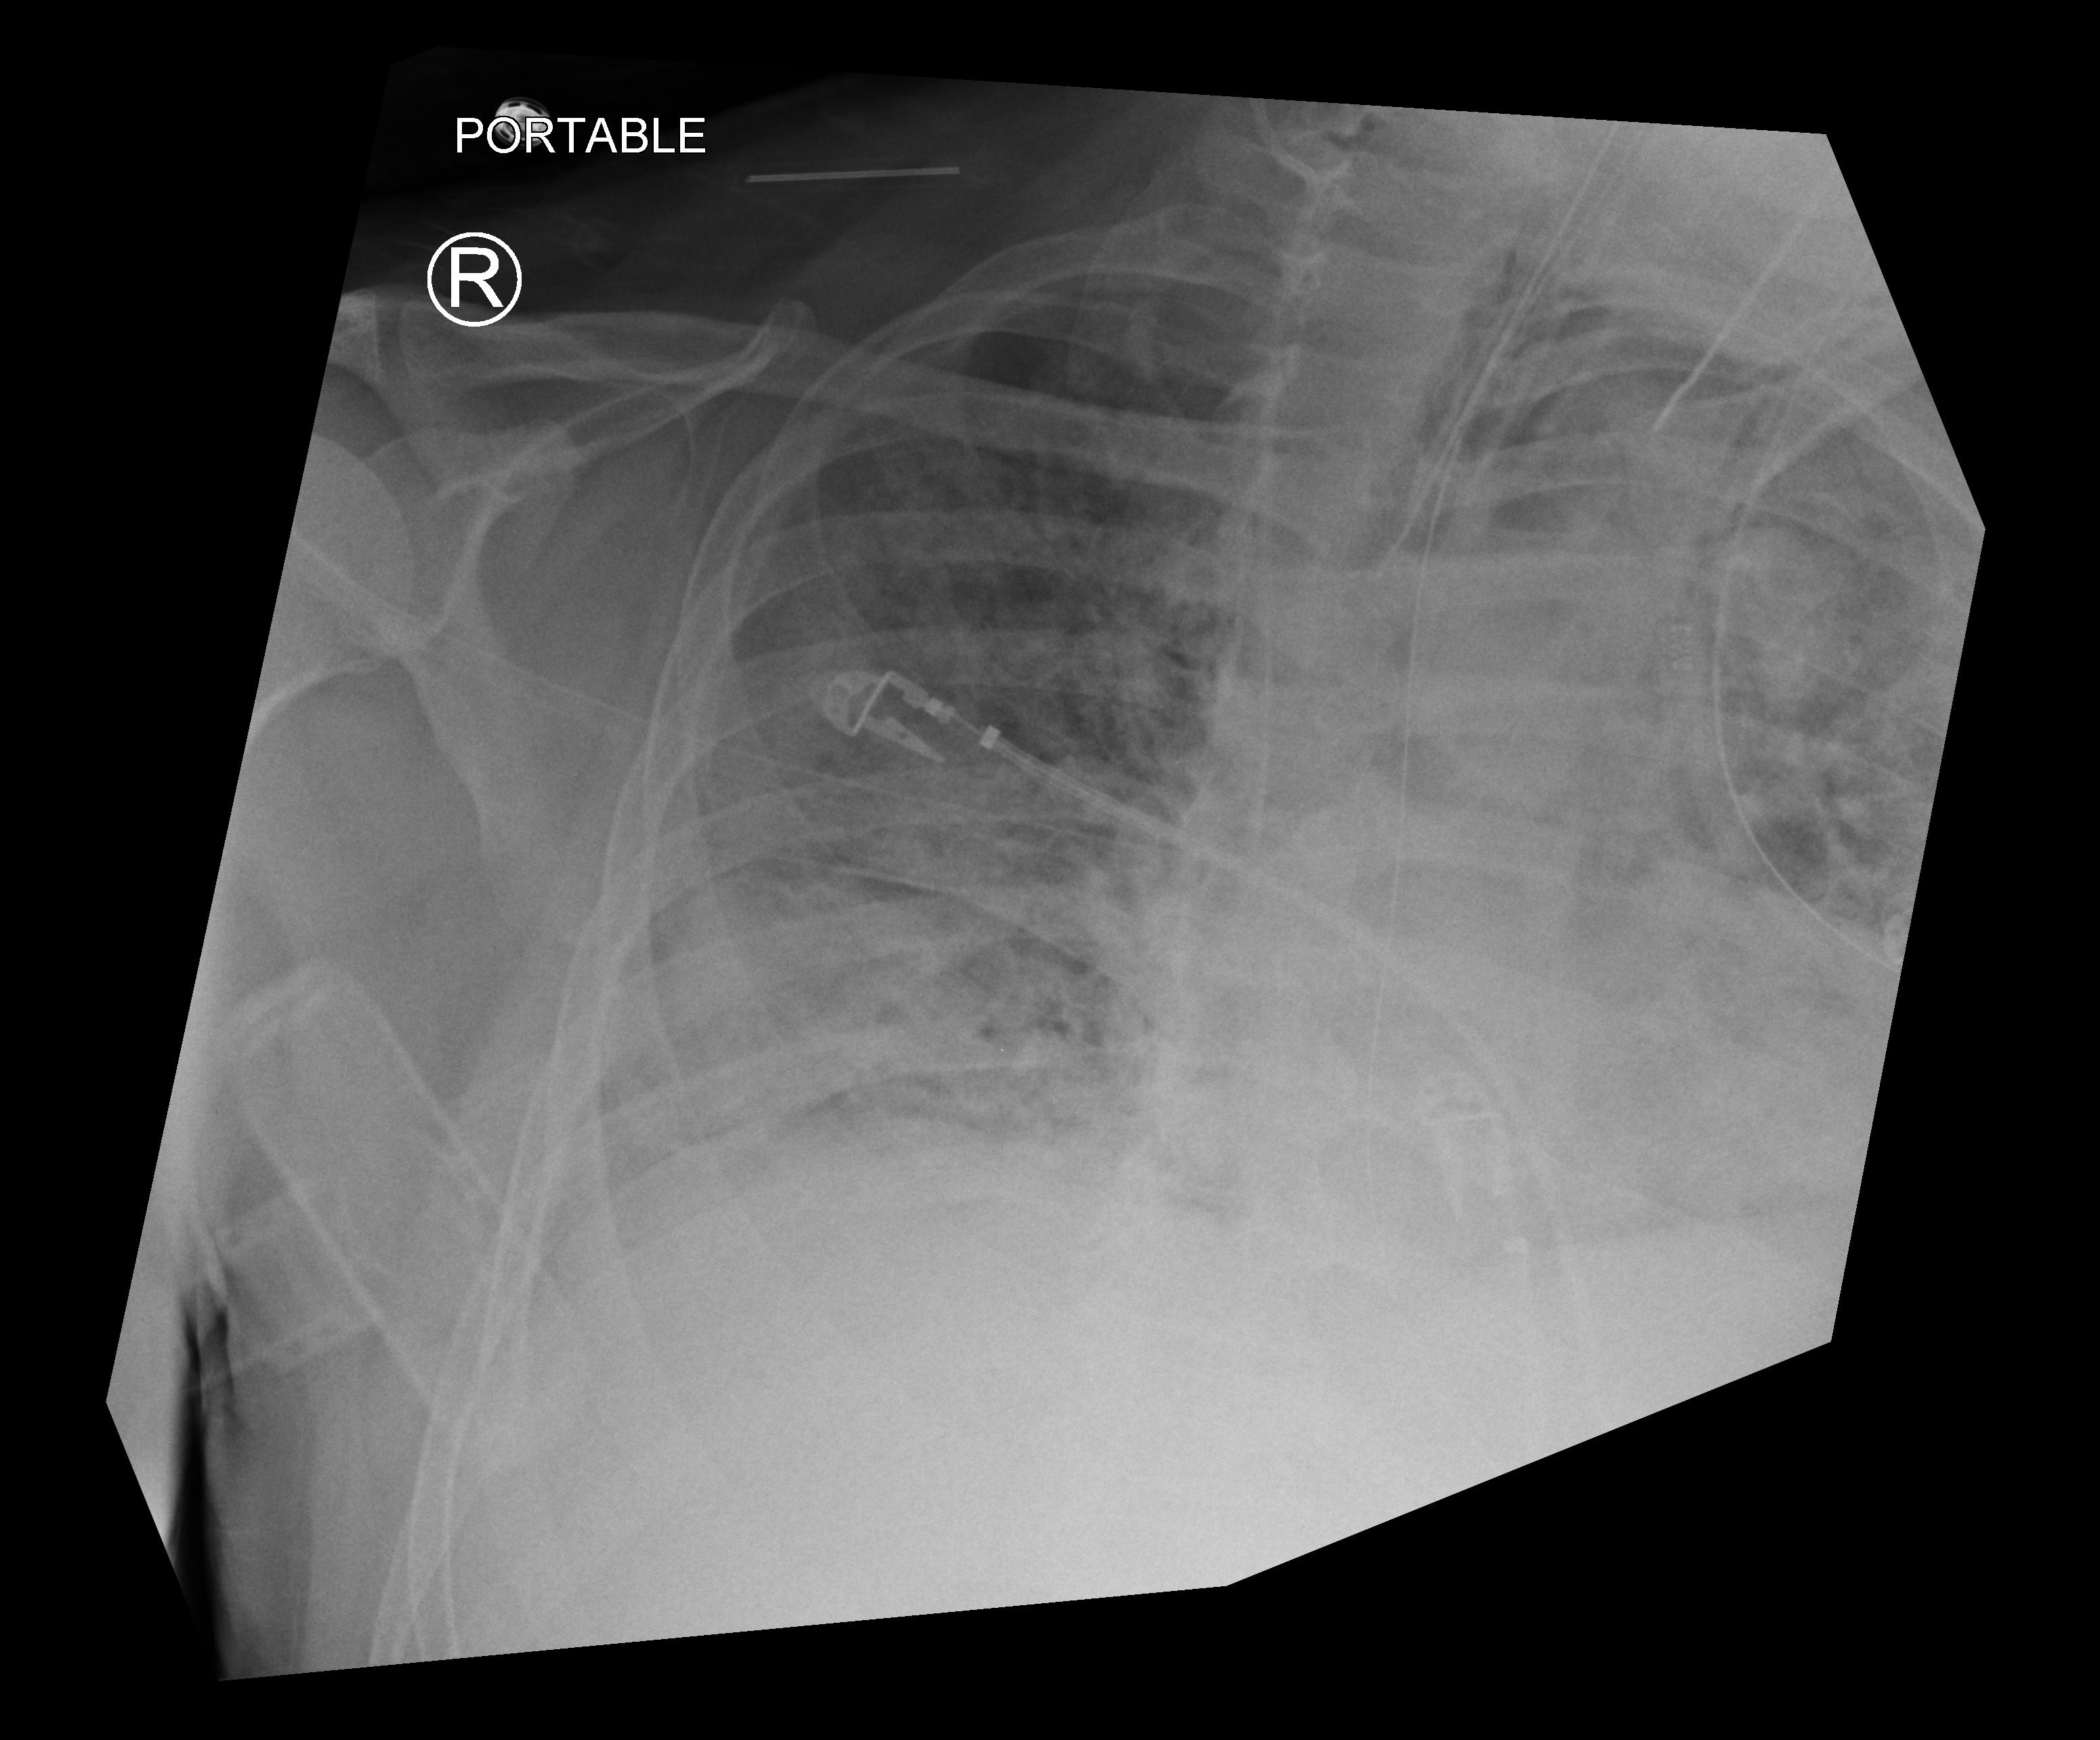
Chest X-ray (portable), anteroposterior (AP) projection. Male patient hospitalised with COVID-19, age 60–74 years.
Admission-level facts for this patient (not findings on this image; timing relative to this image not recorded): COPD (admission record): no.